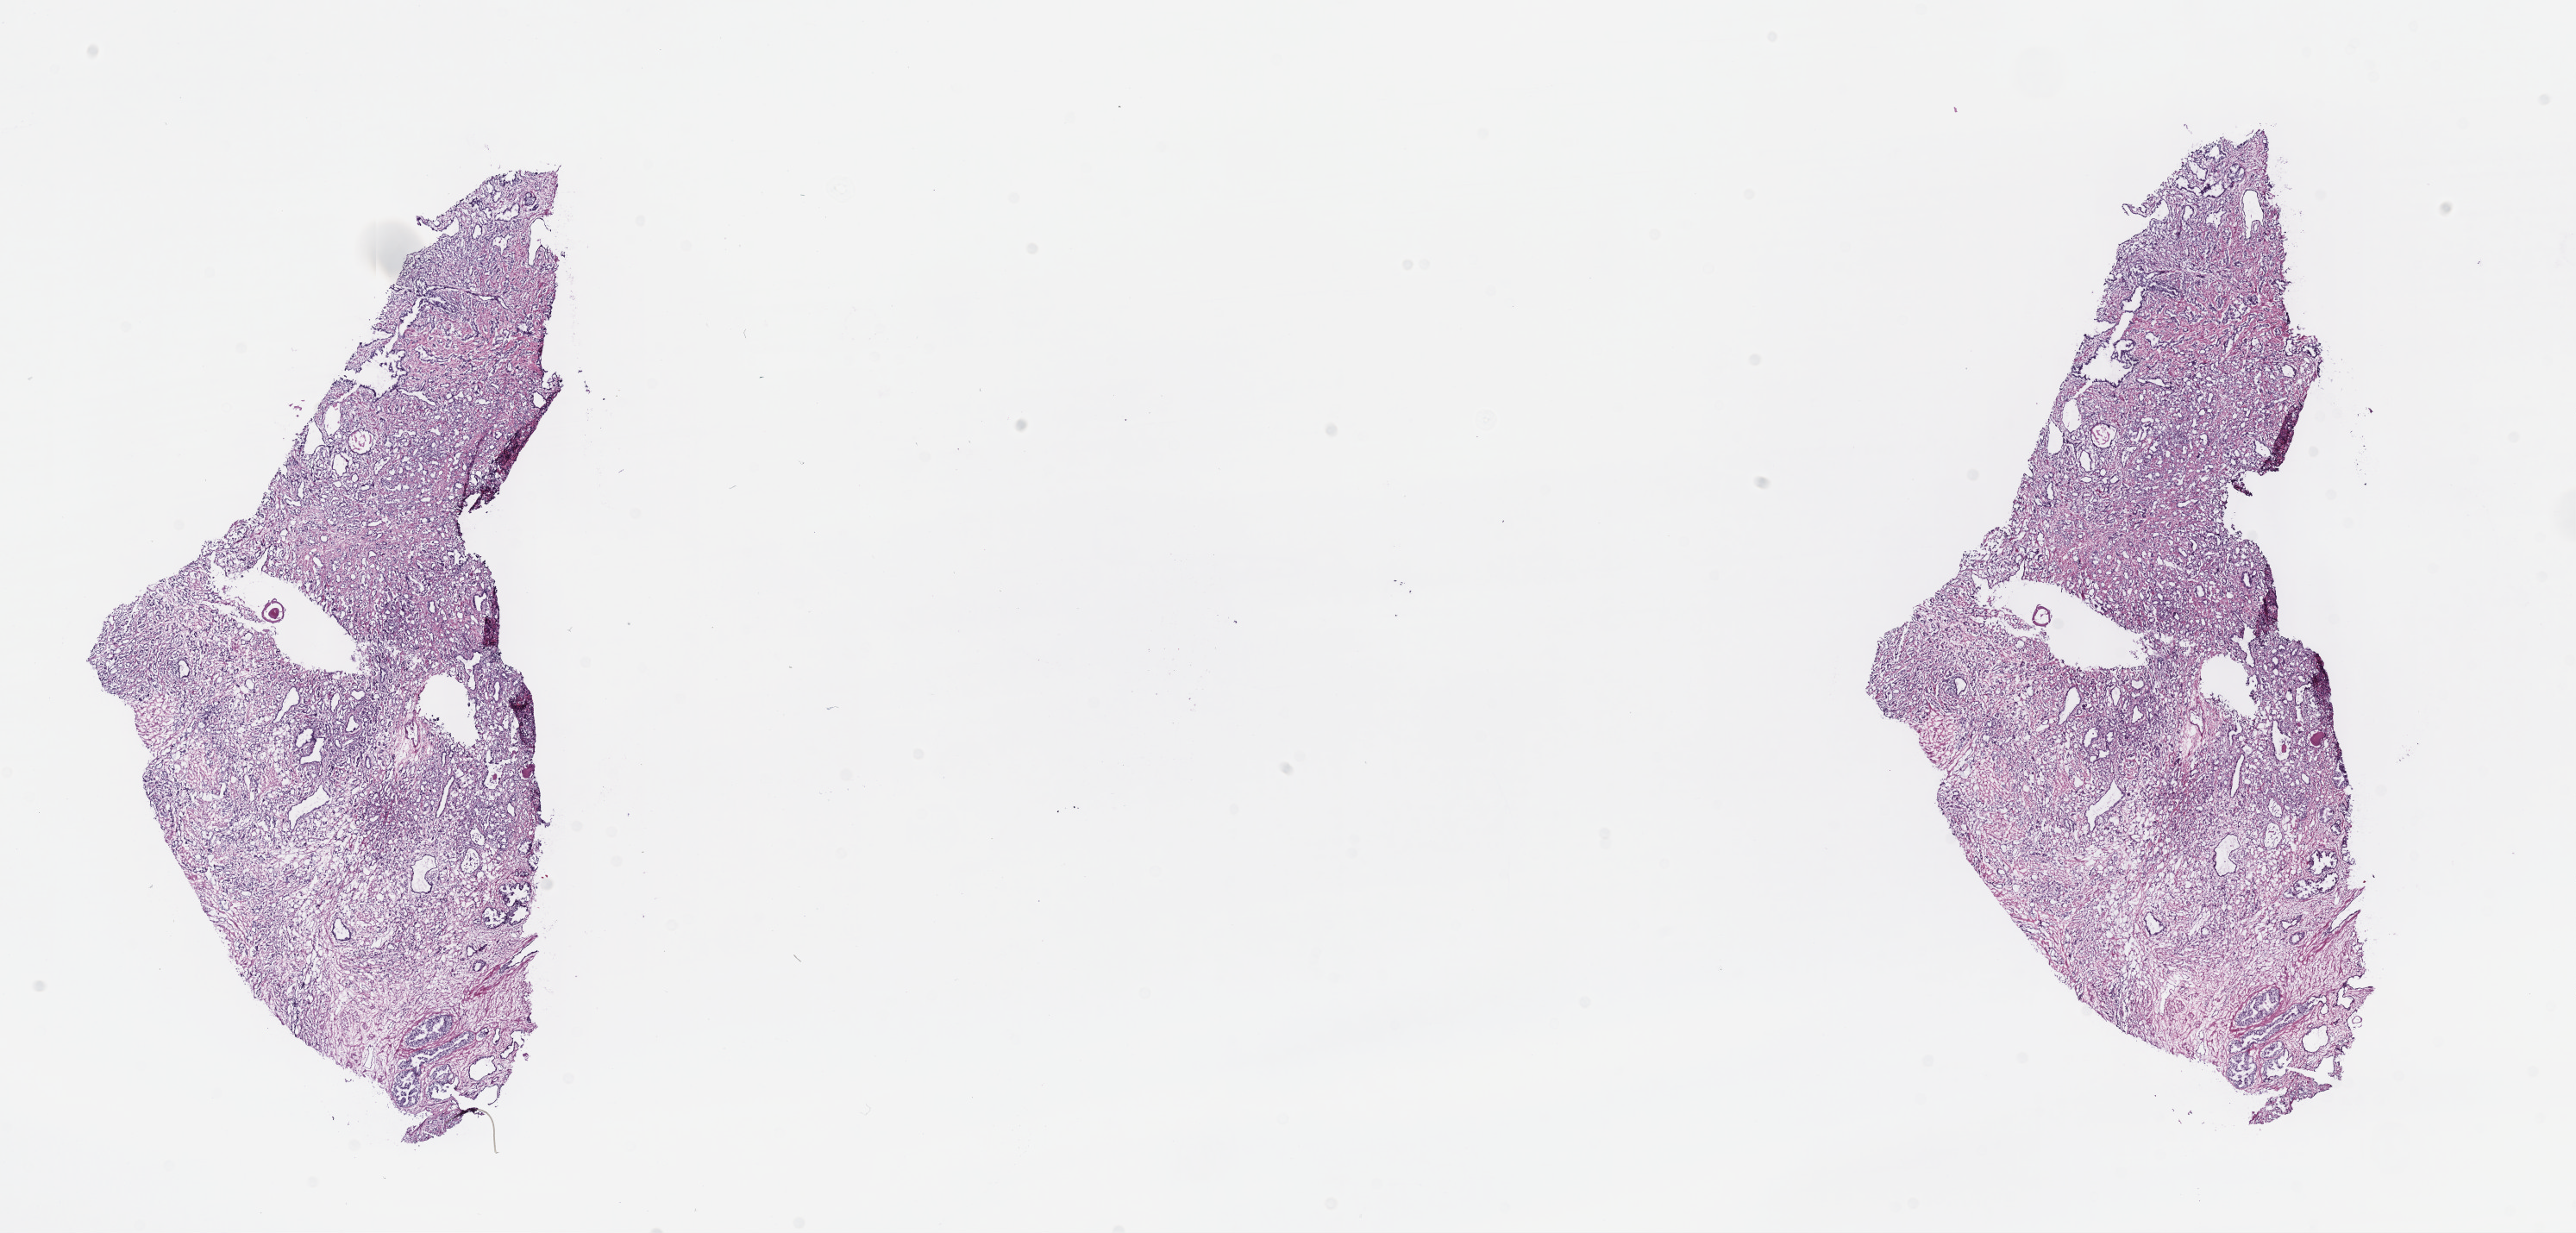
Whole-slide histology image, Hematoxylin and eosin (H&E) stained — shown as a low-resolution overview of the whole scanned area (about 24.2 x 11.6 mm, acquisition: 40x scan); frozen section from the top of the tissue portion; prostate, primary tumour sample. Male, age 65 years at initial diagnosis.
Diagnosis: Adenocarcinoma, NOS (prostate gland).